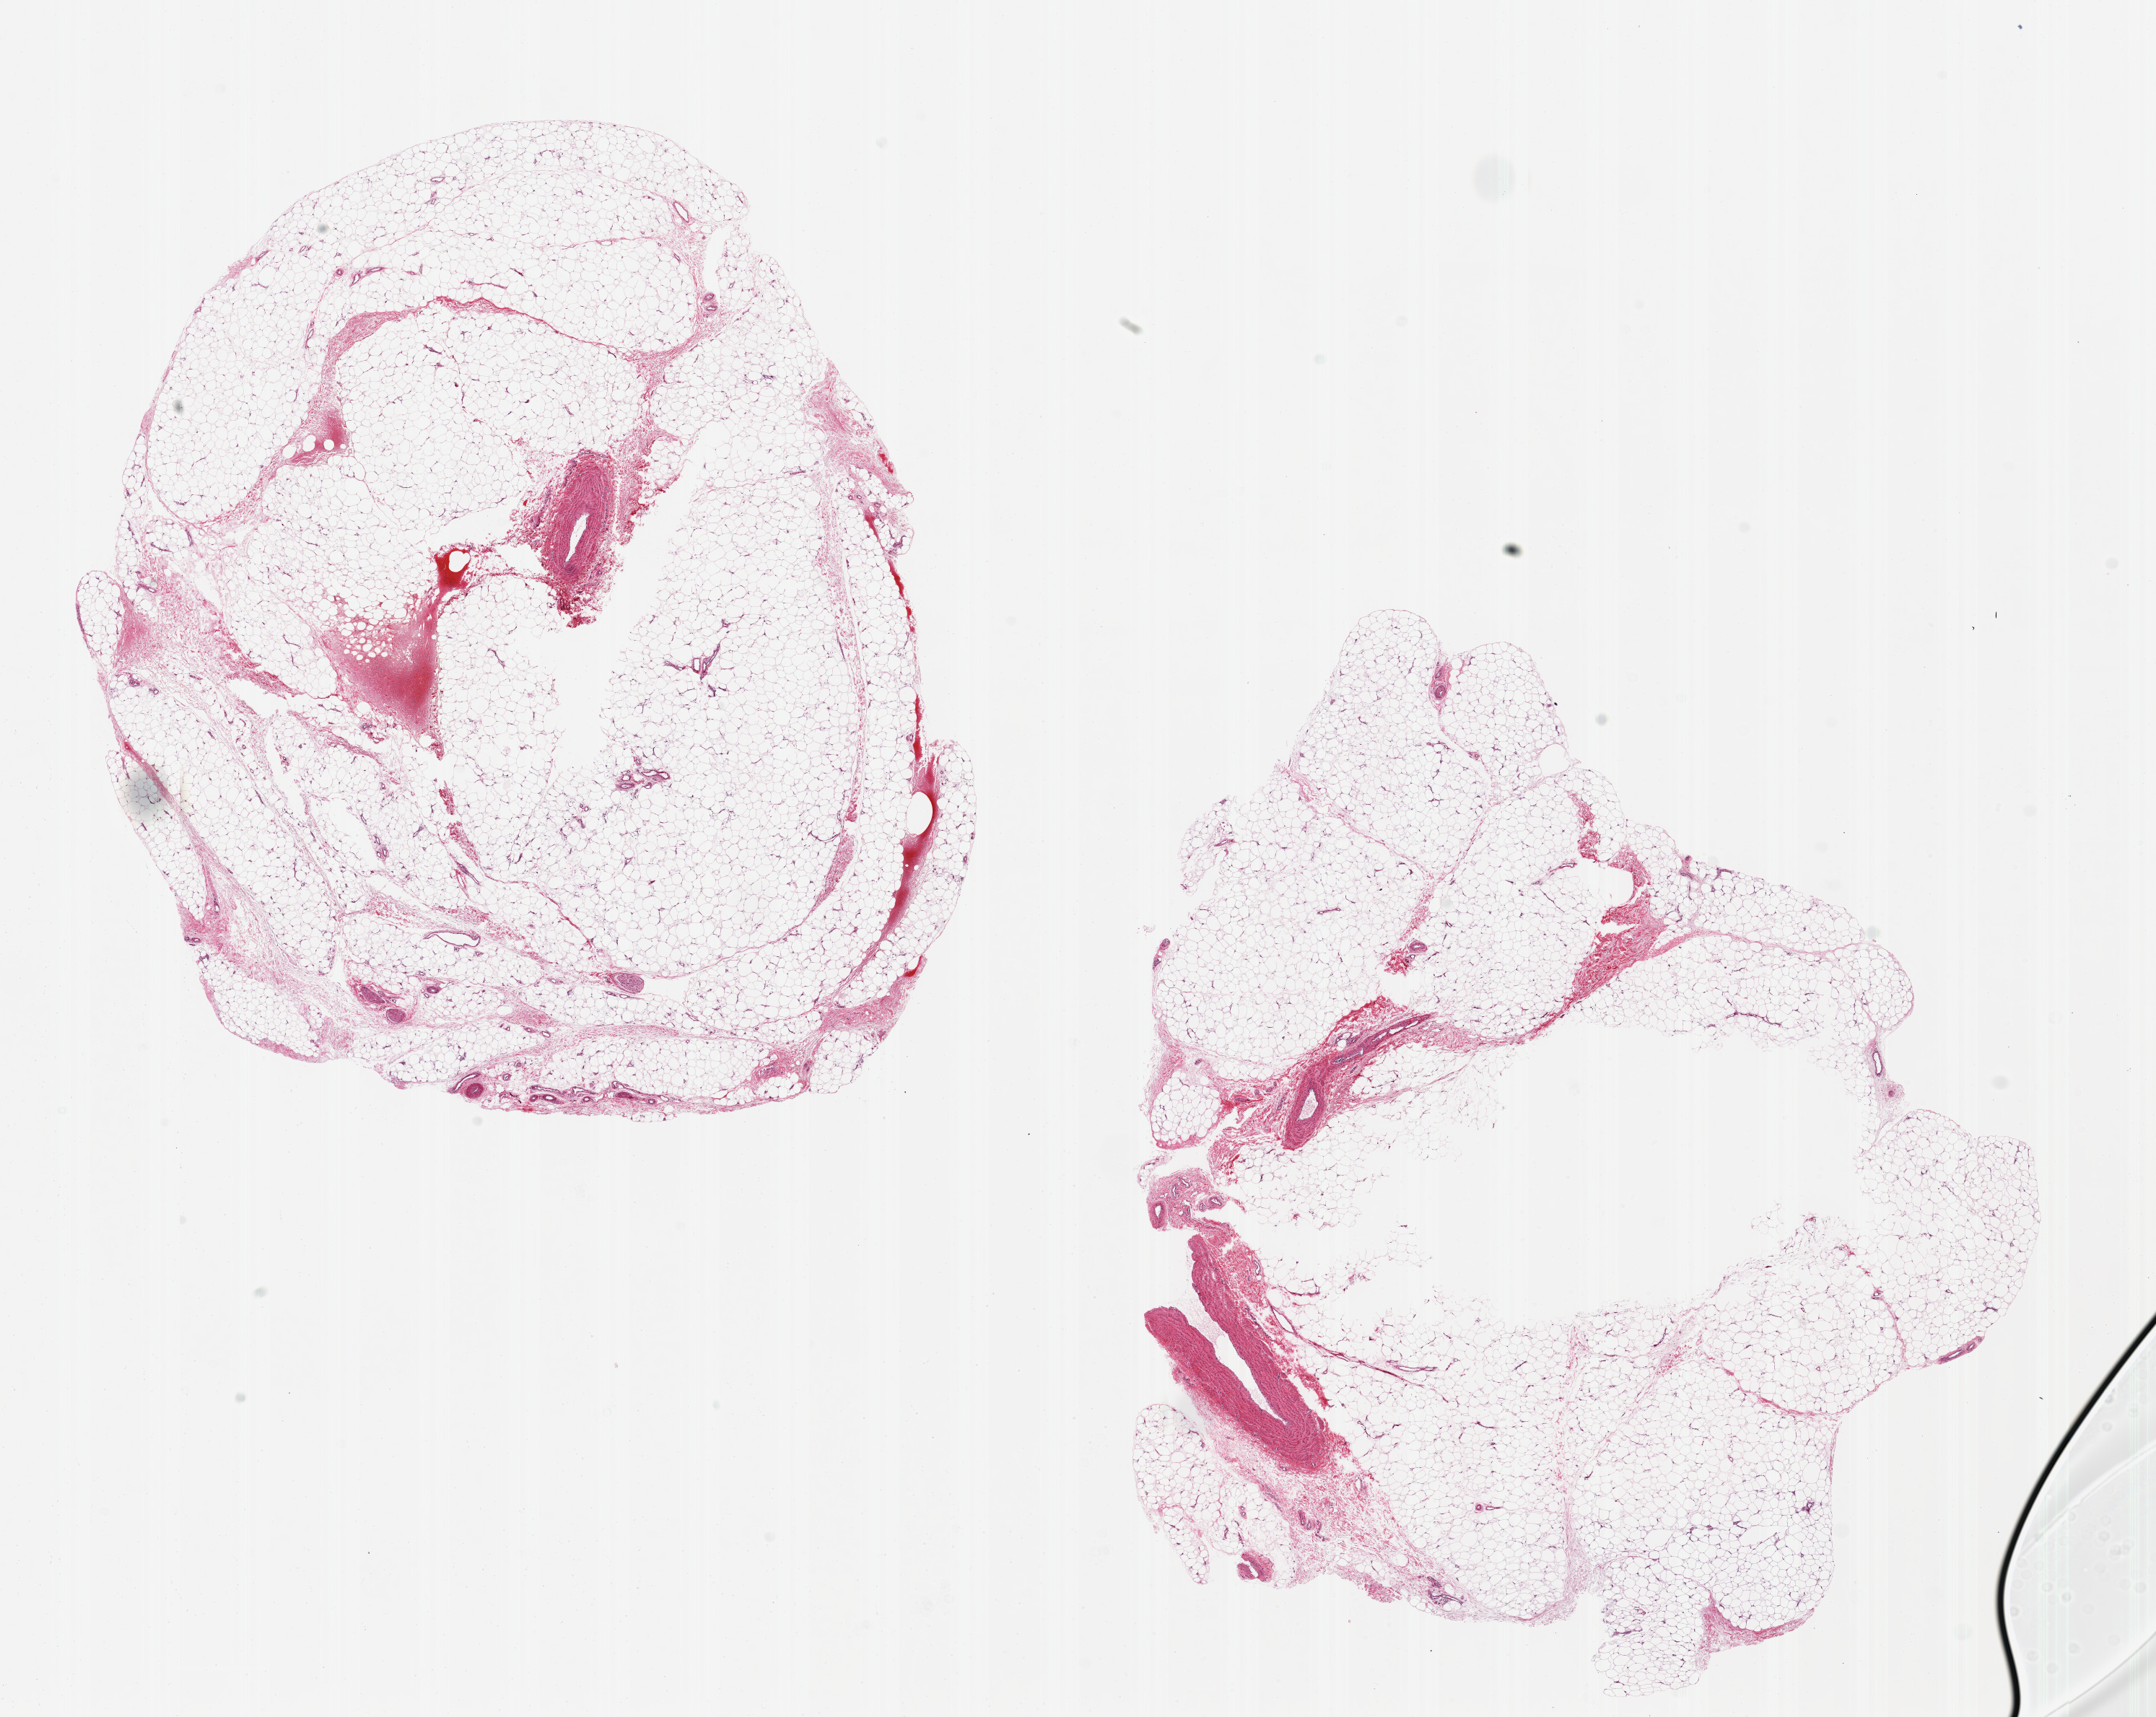
Haematoxylin and eosin whole-slide image — whole scanned area (about 23.6 x 18.8 mm) shown as a low-resolution overview, PAXgene-fixed paraffin-embedded (PFPE) section, section of adipose tissue (target tissue), tissue donor sample. Donor: male.
Reviewer comment on this tissue sample: 2 pieces ~11x8 mm.